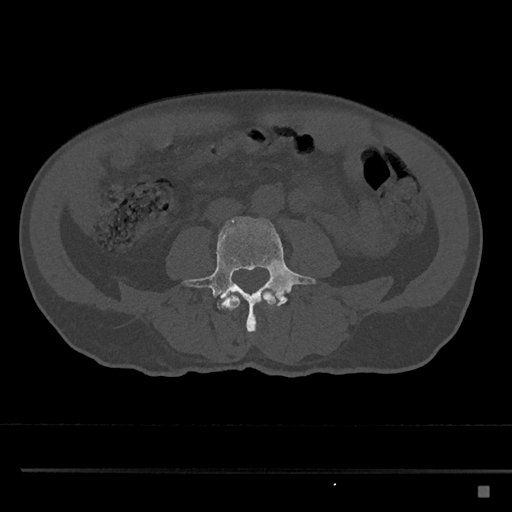
CT including the spine, one axial slice. Position 649 of 797 along the scan axis. Reconstruction kernel Br40s/3. 120 kVp. Bone window (W 1800 / L 400 HU). 512 × 512 image matrix, field of view 391 × 391 mm. Patient: male, 59 years. From the clinical record (not read from this slice): primary cancer: prostate.
Structures marked on this image (semi-automatically segmented with operator editing):
- L3 vertebra: bounding box [x1, y1, x2, y2] px = [222, 291, 277, 319]
- L4 vertebra: [182, 217, 316, 336]